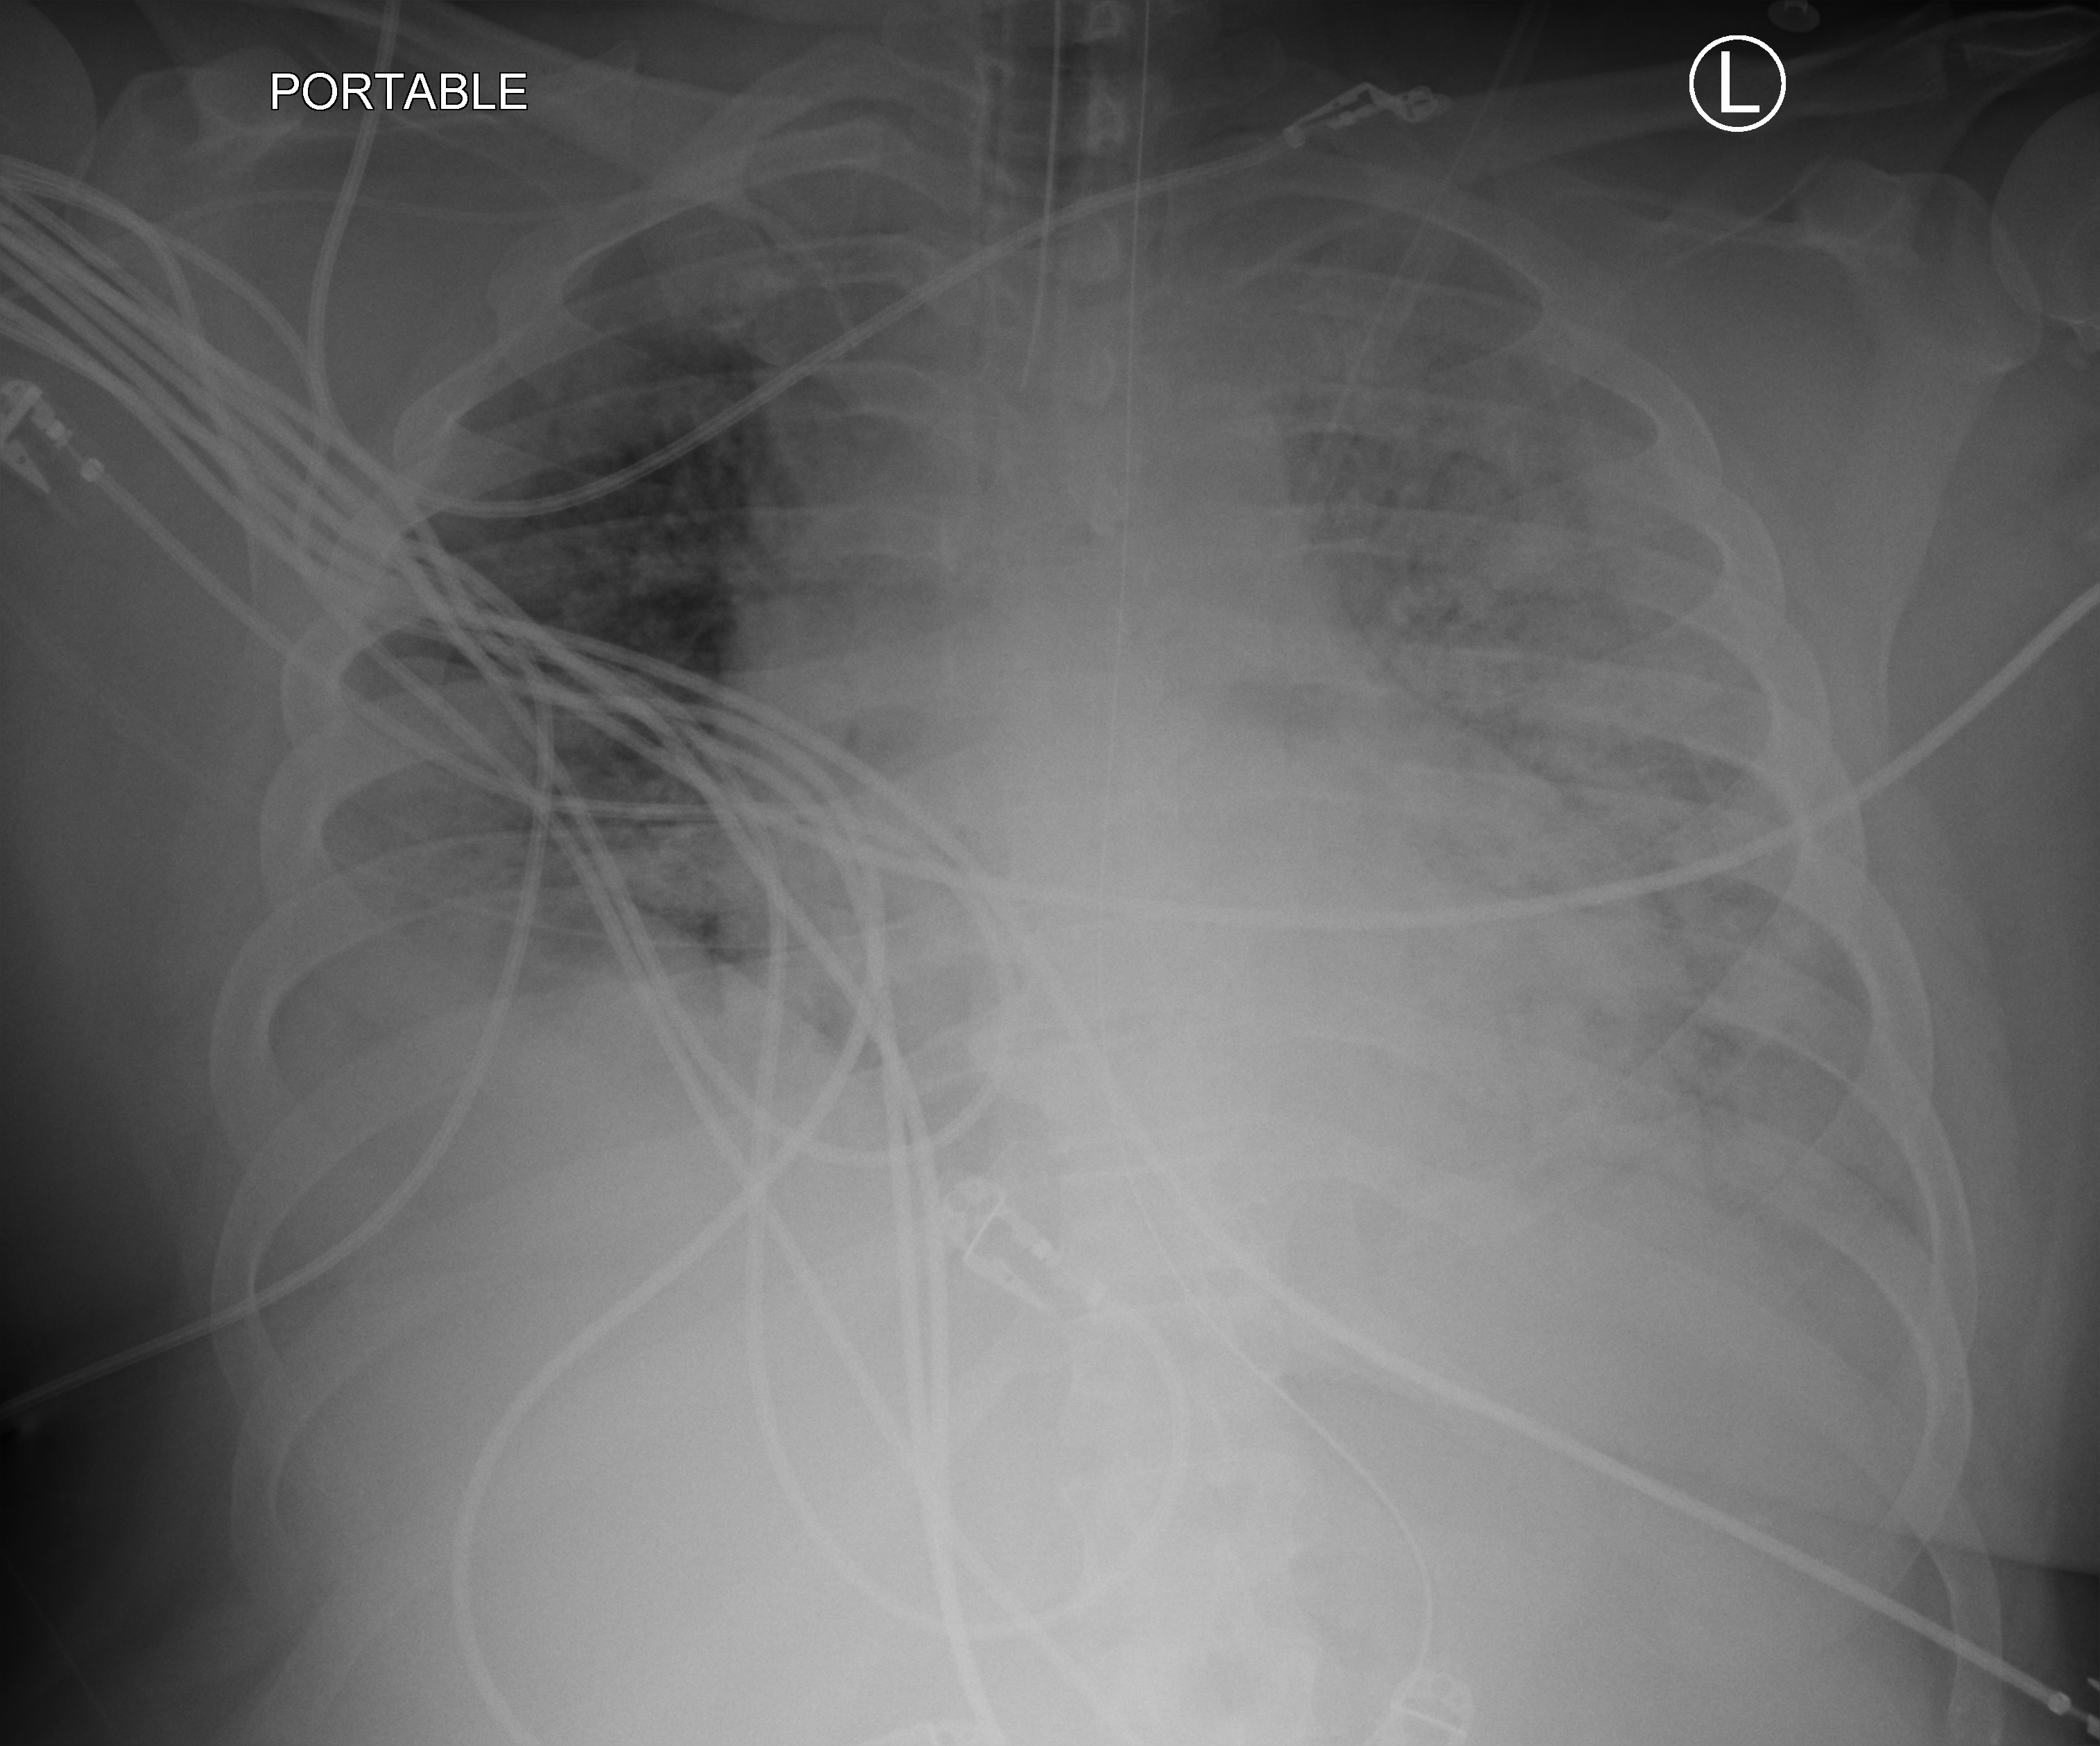
Chest X-ray (portable); anteroposterior (AP) projection. Adult patient hospitalised with COVID-19, age 18–59 years.
Hospital-stay facts (about this admission, not read from this image; timing relative to this image not recorded): admitted to intensive care during this hospital stay: yes; mechanically ventilated during this hospital stay: yes; length of hospital stay: 10 days.